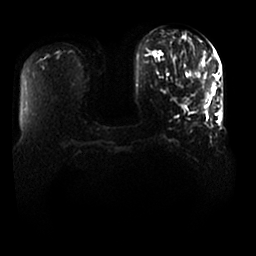
Breast MRI, one axial slice. Position 4 of 25 along the scan axis. Diffusion-weighted series; image 2 of 4 stored at this slice position (different b-values; order by instance number). 1.5 T. 4 mm slice thickness. 256 × 256 image matrix. Female patient.
Annotated regions visible in this slice (expert manual segmentation):
- tumour on diffusion-weighted imaging: bounding box <206,89,215,98> (left, top, right, bottom; pixels)